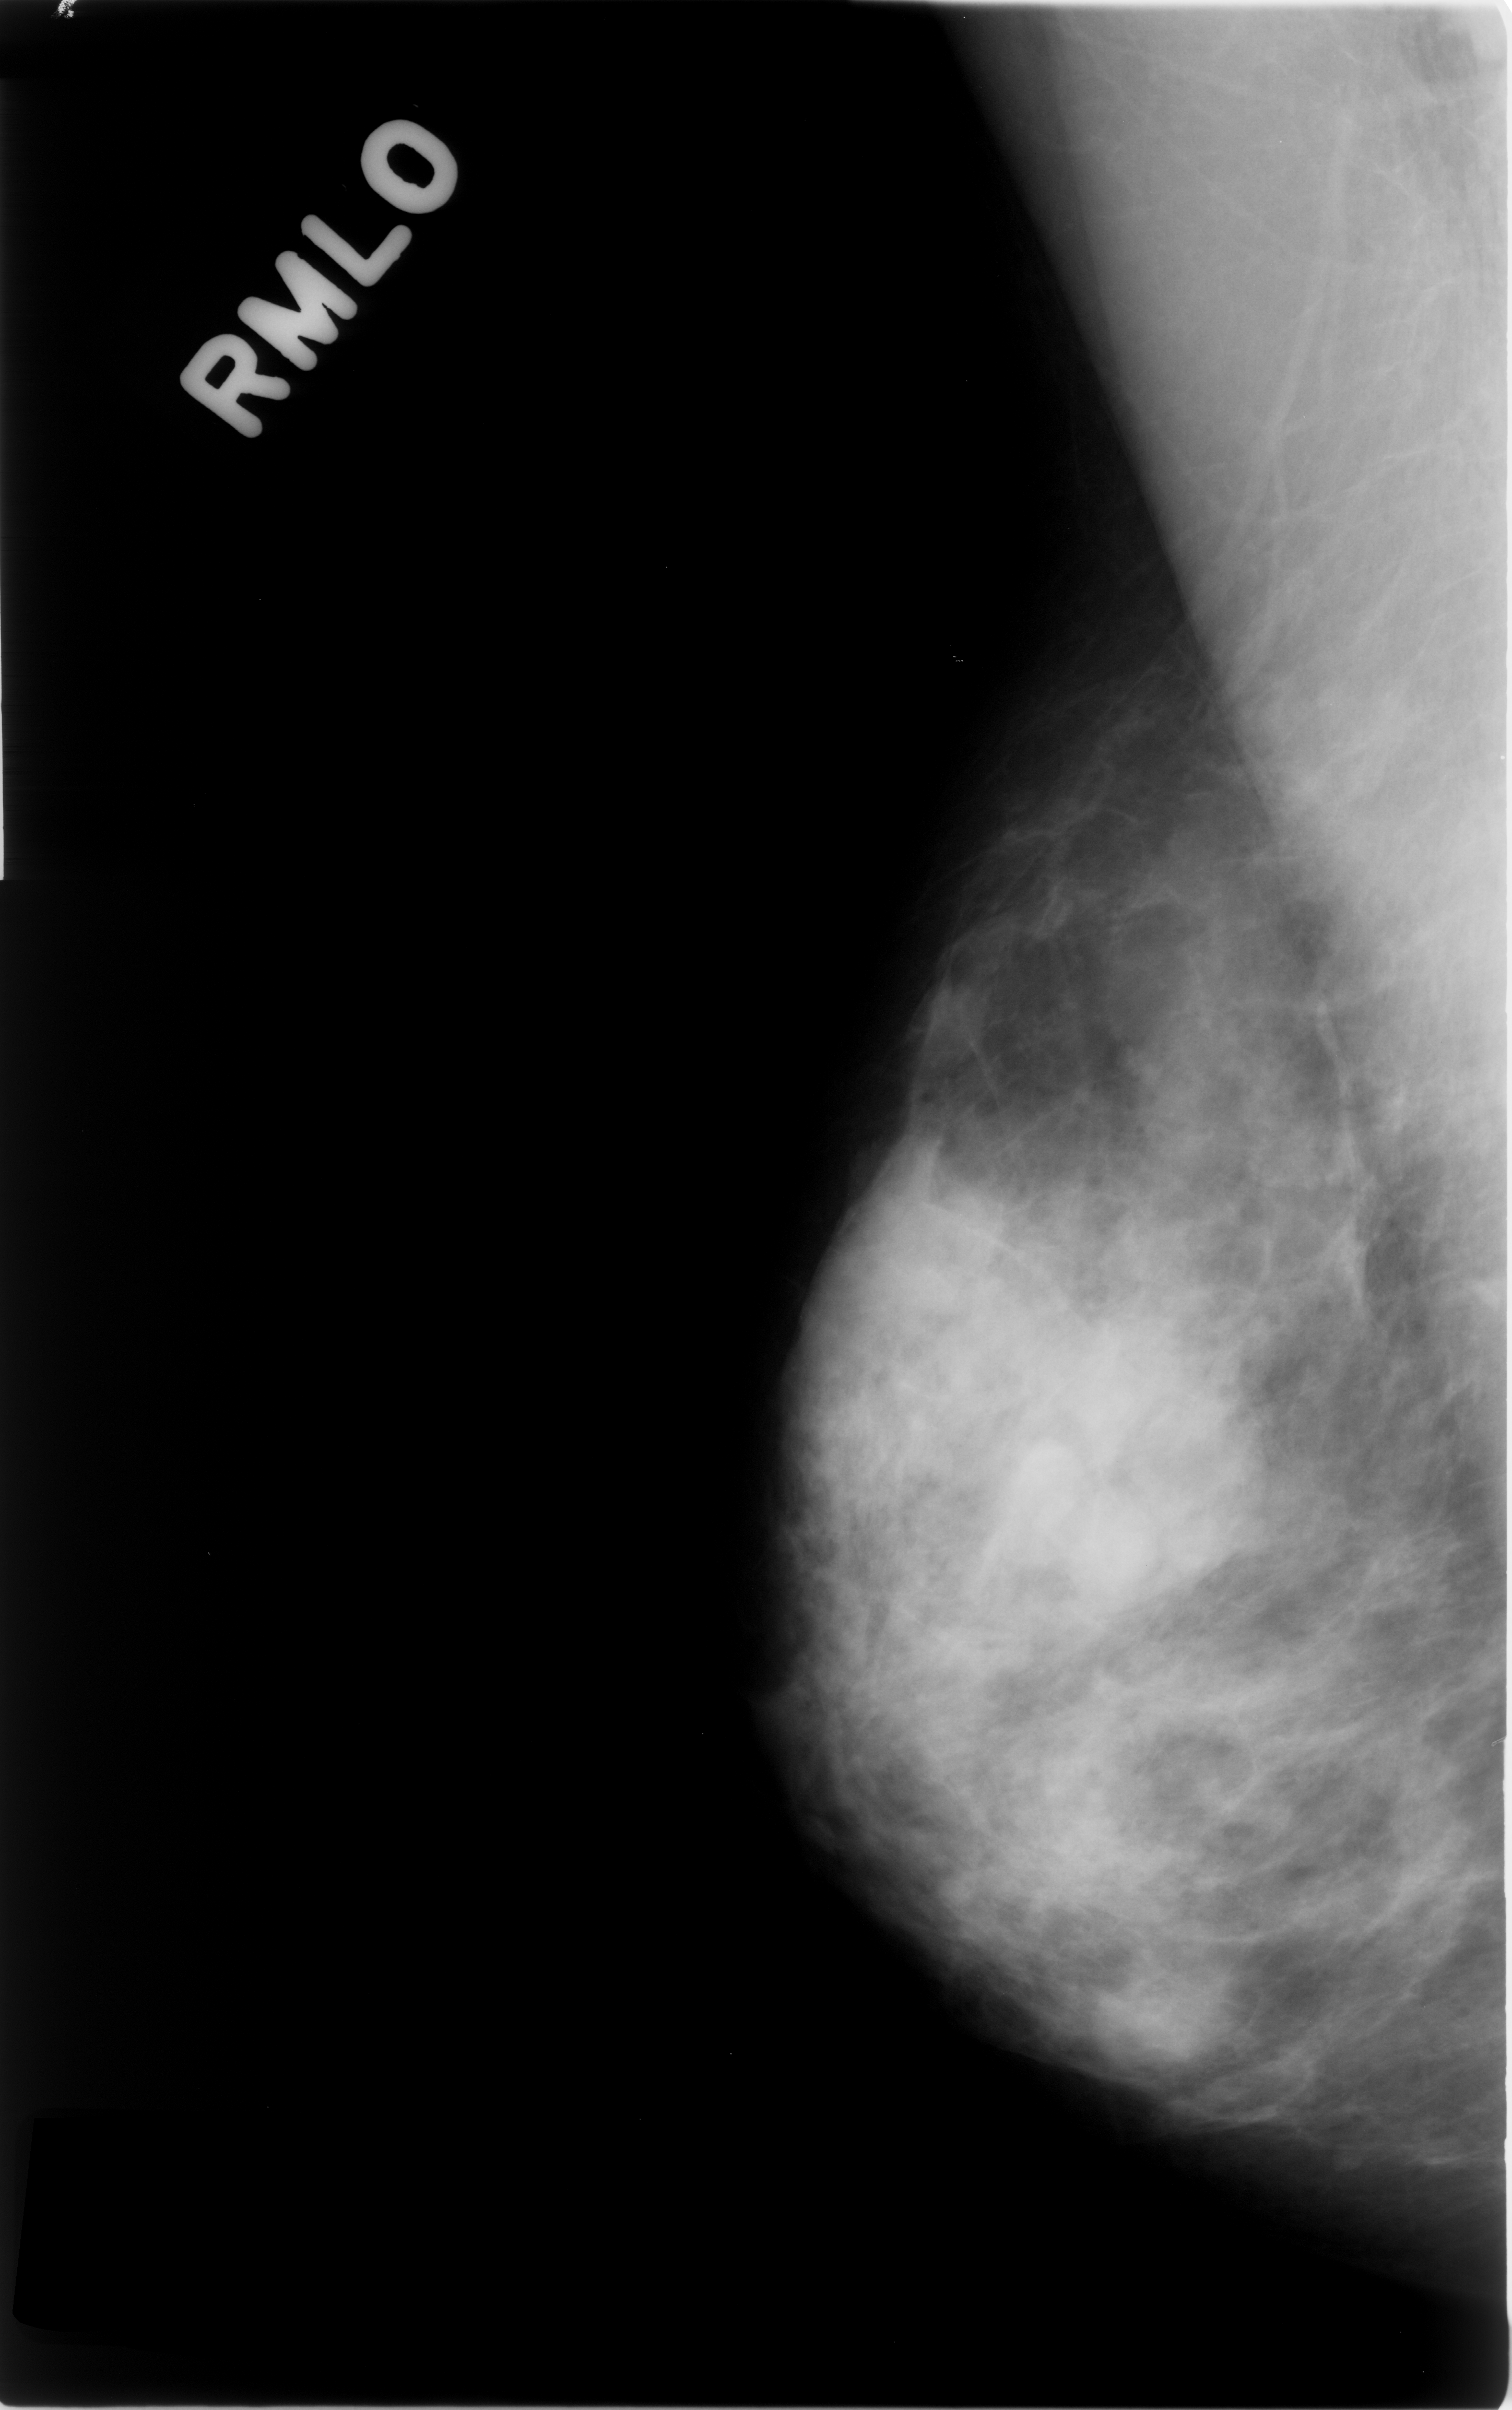
Scanned film-screen mammogram, right breast, mediolateral oblique (MLO) view, BI-RADS breast density category 3 (scale 1–4).
Radiologist-marked abnormalities on this image: mass, shape lobulated, margins obscured; BI-RADS assessment category 3; pathology (as recorded): benign.